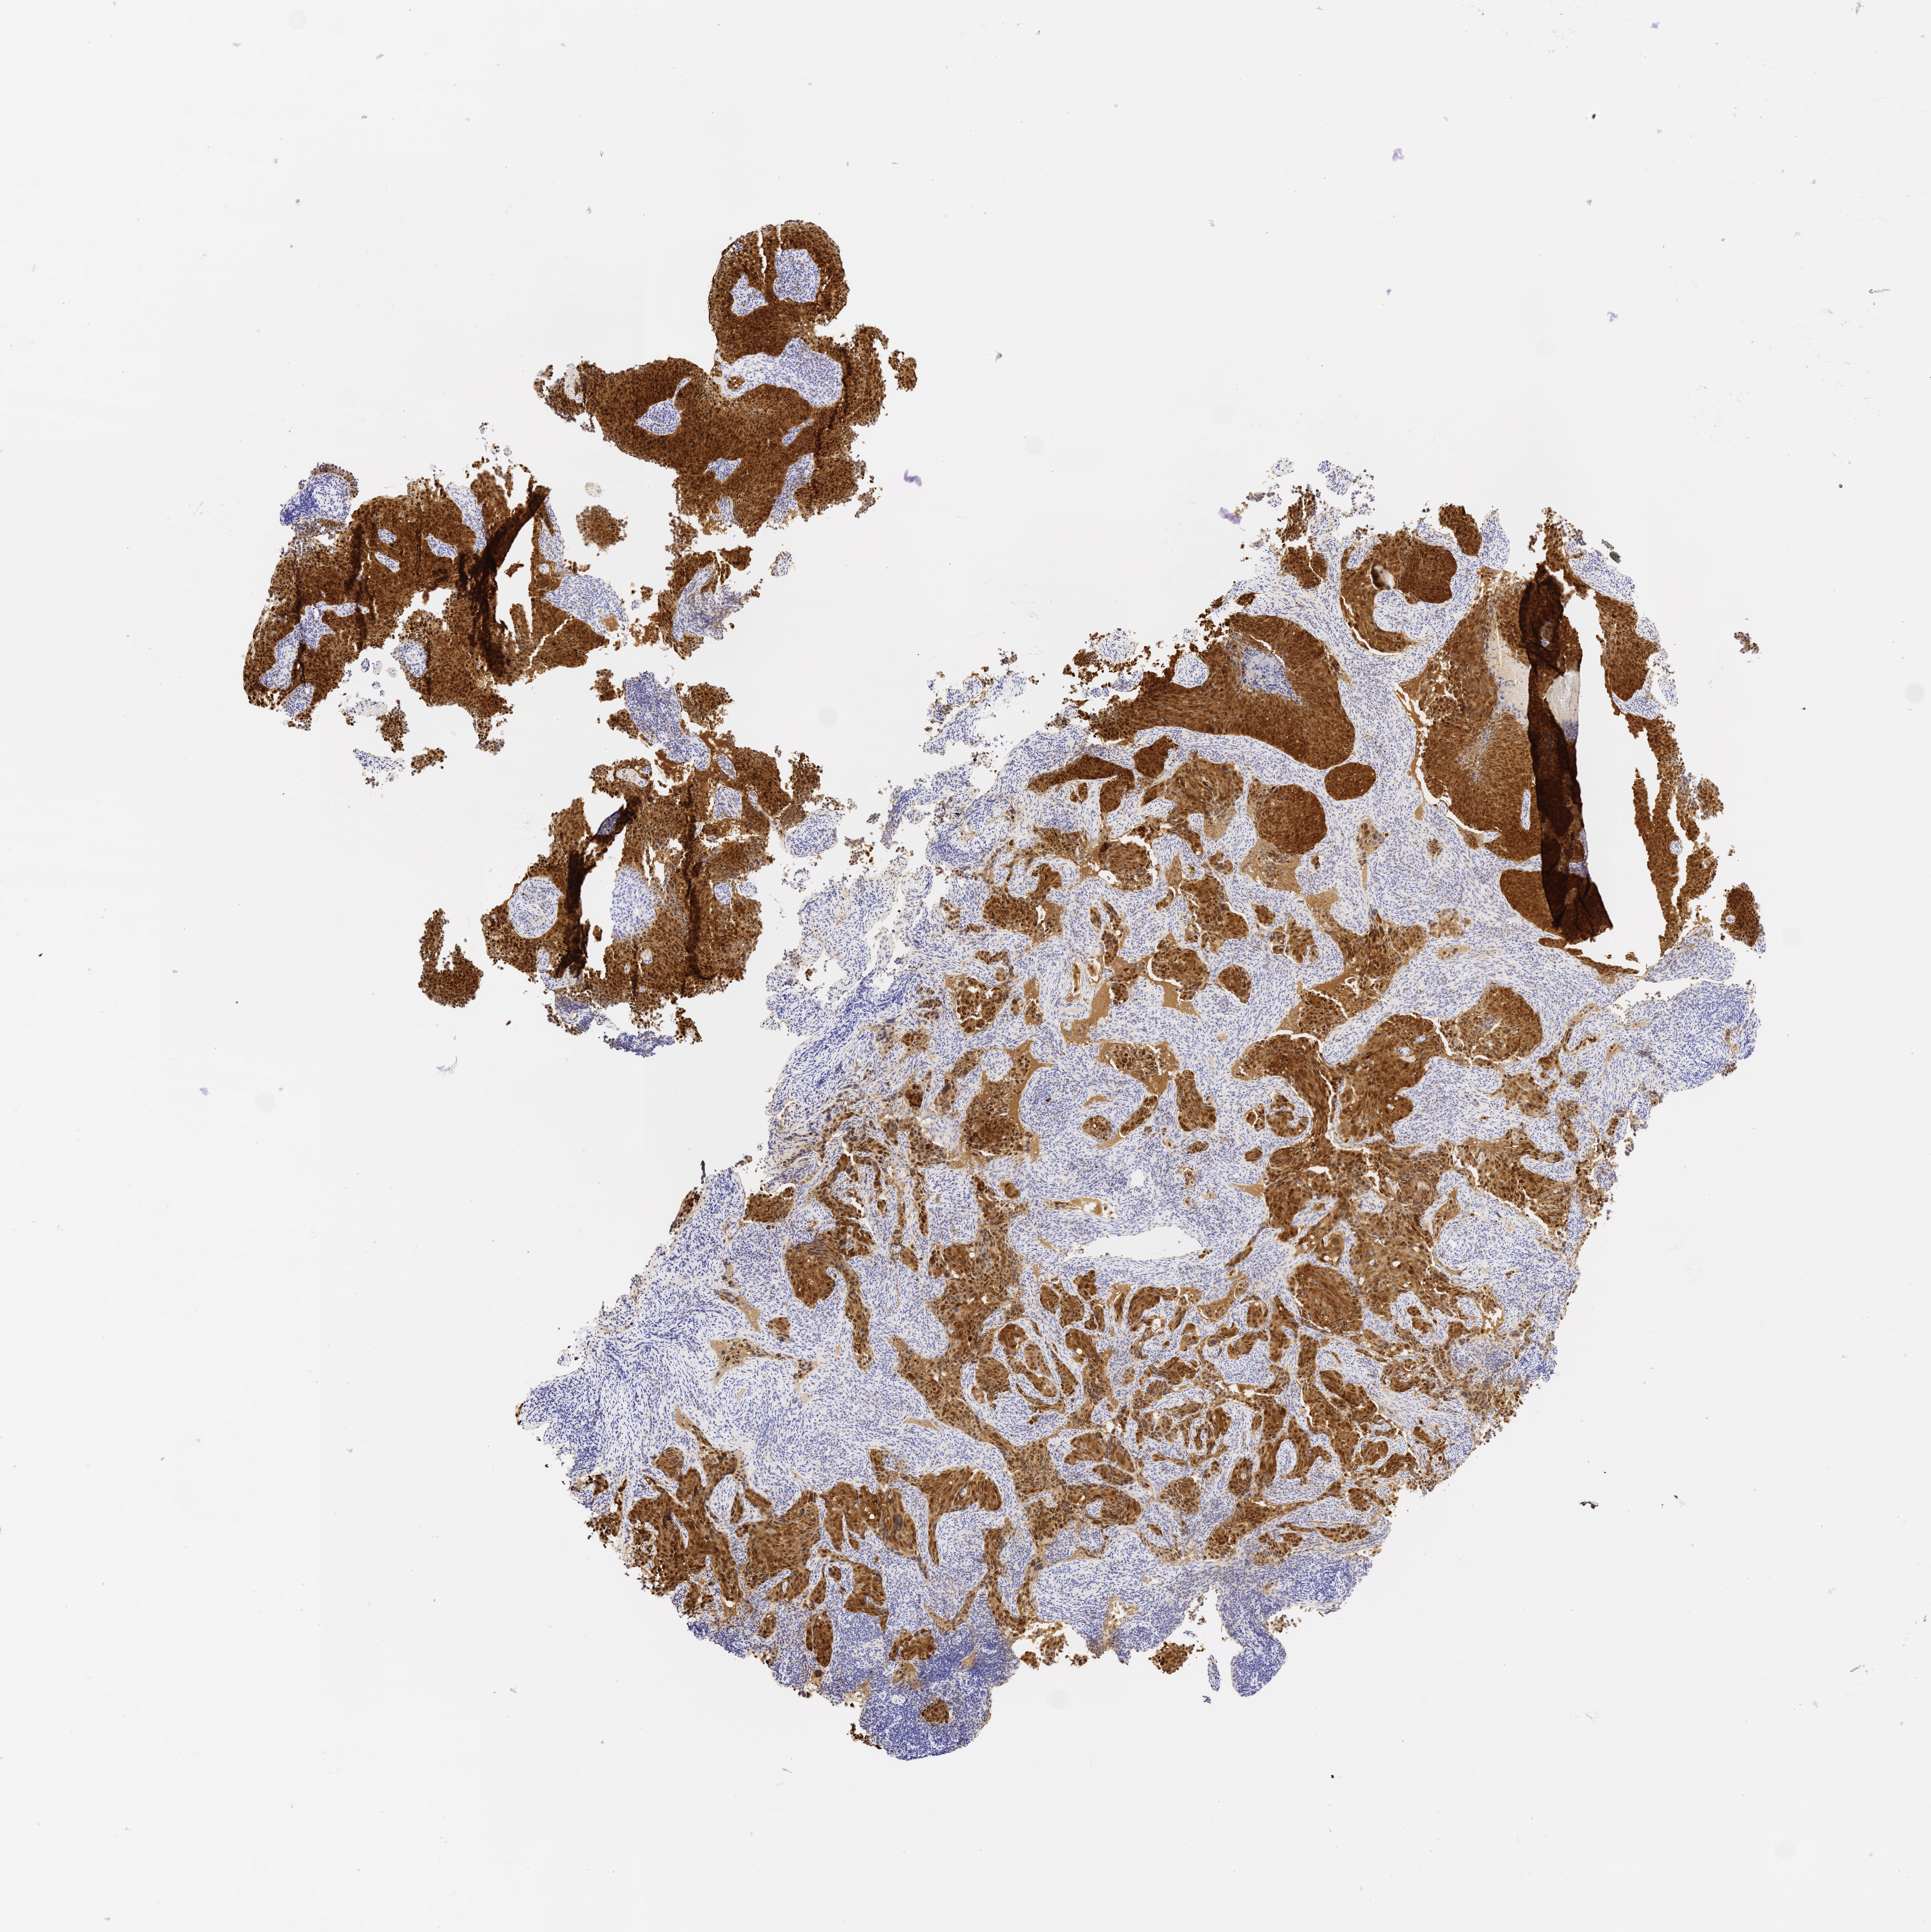
IHC for p16 (p16INK4a), whole-slide image — whole scanned area (about 6.0 x 6.0 mm) shown as a low-resolution overview, tumor tissue, anatomic site: cervix. Patient: female, aged 47.
Diagnosis: Squamous cell carcinoma, large cell, nonkeratinizing, NOS.